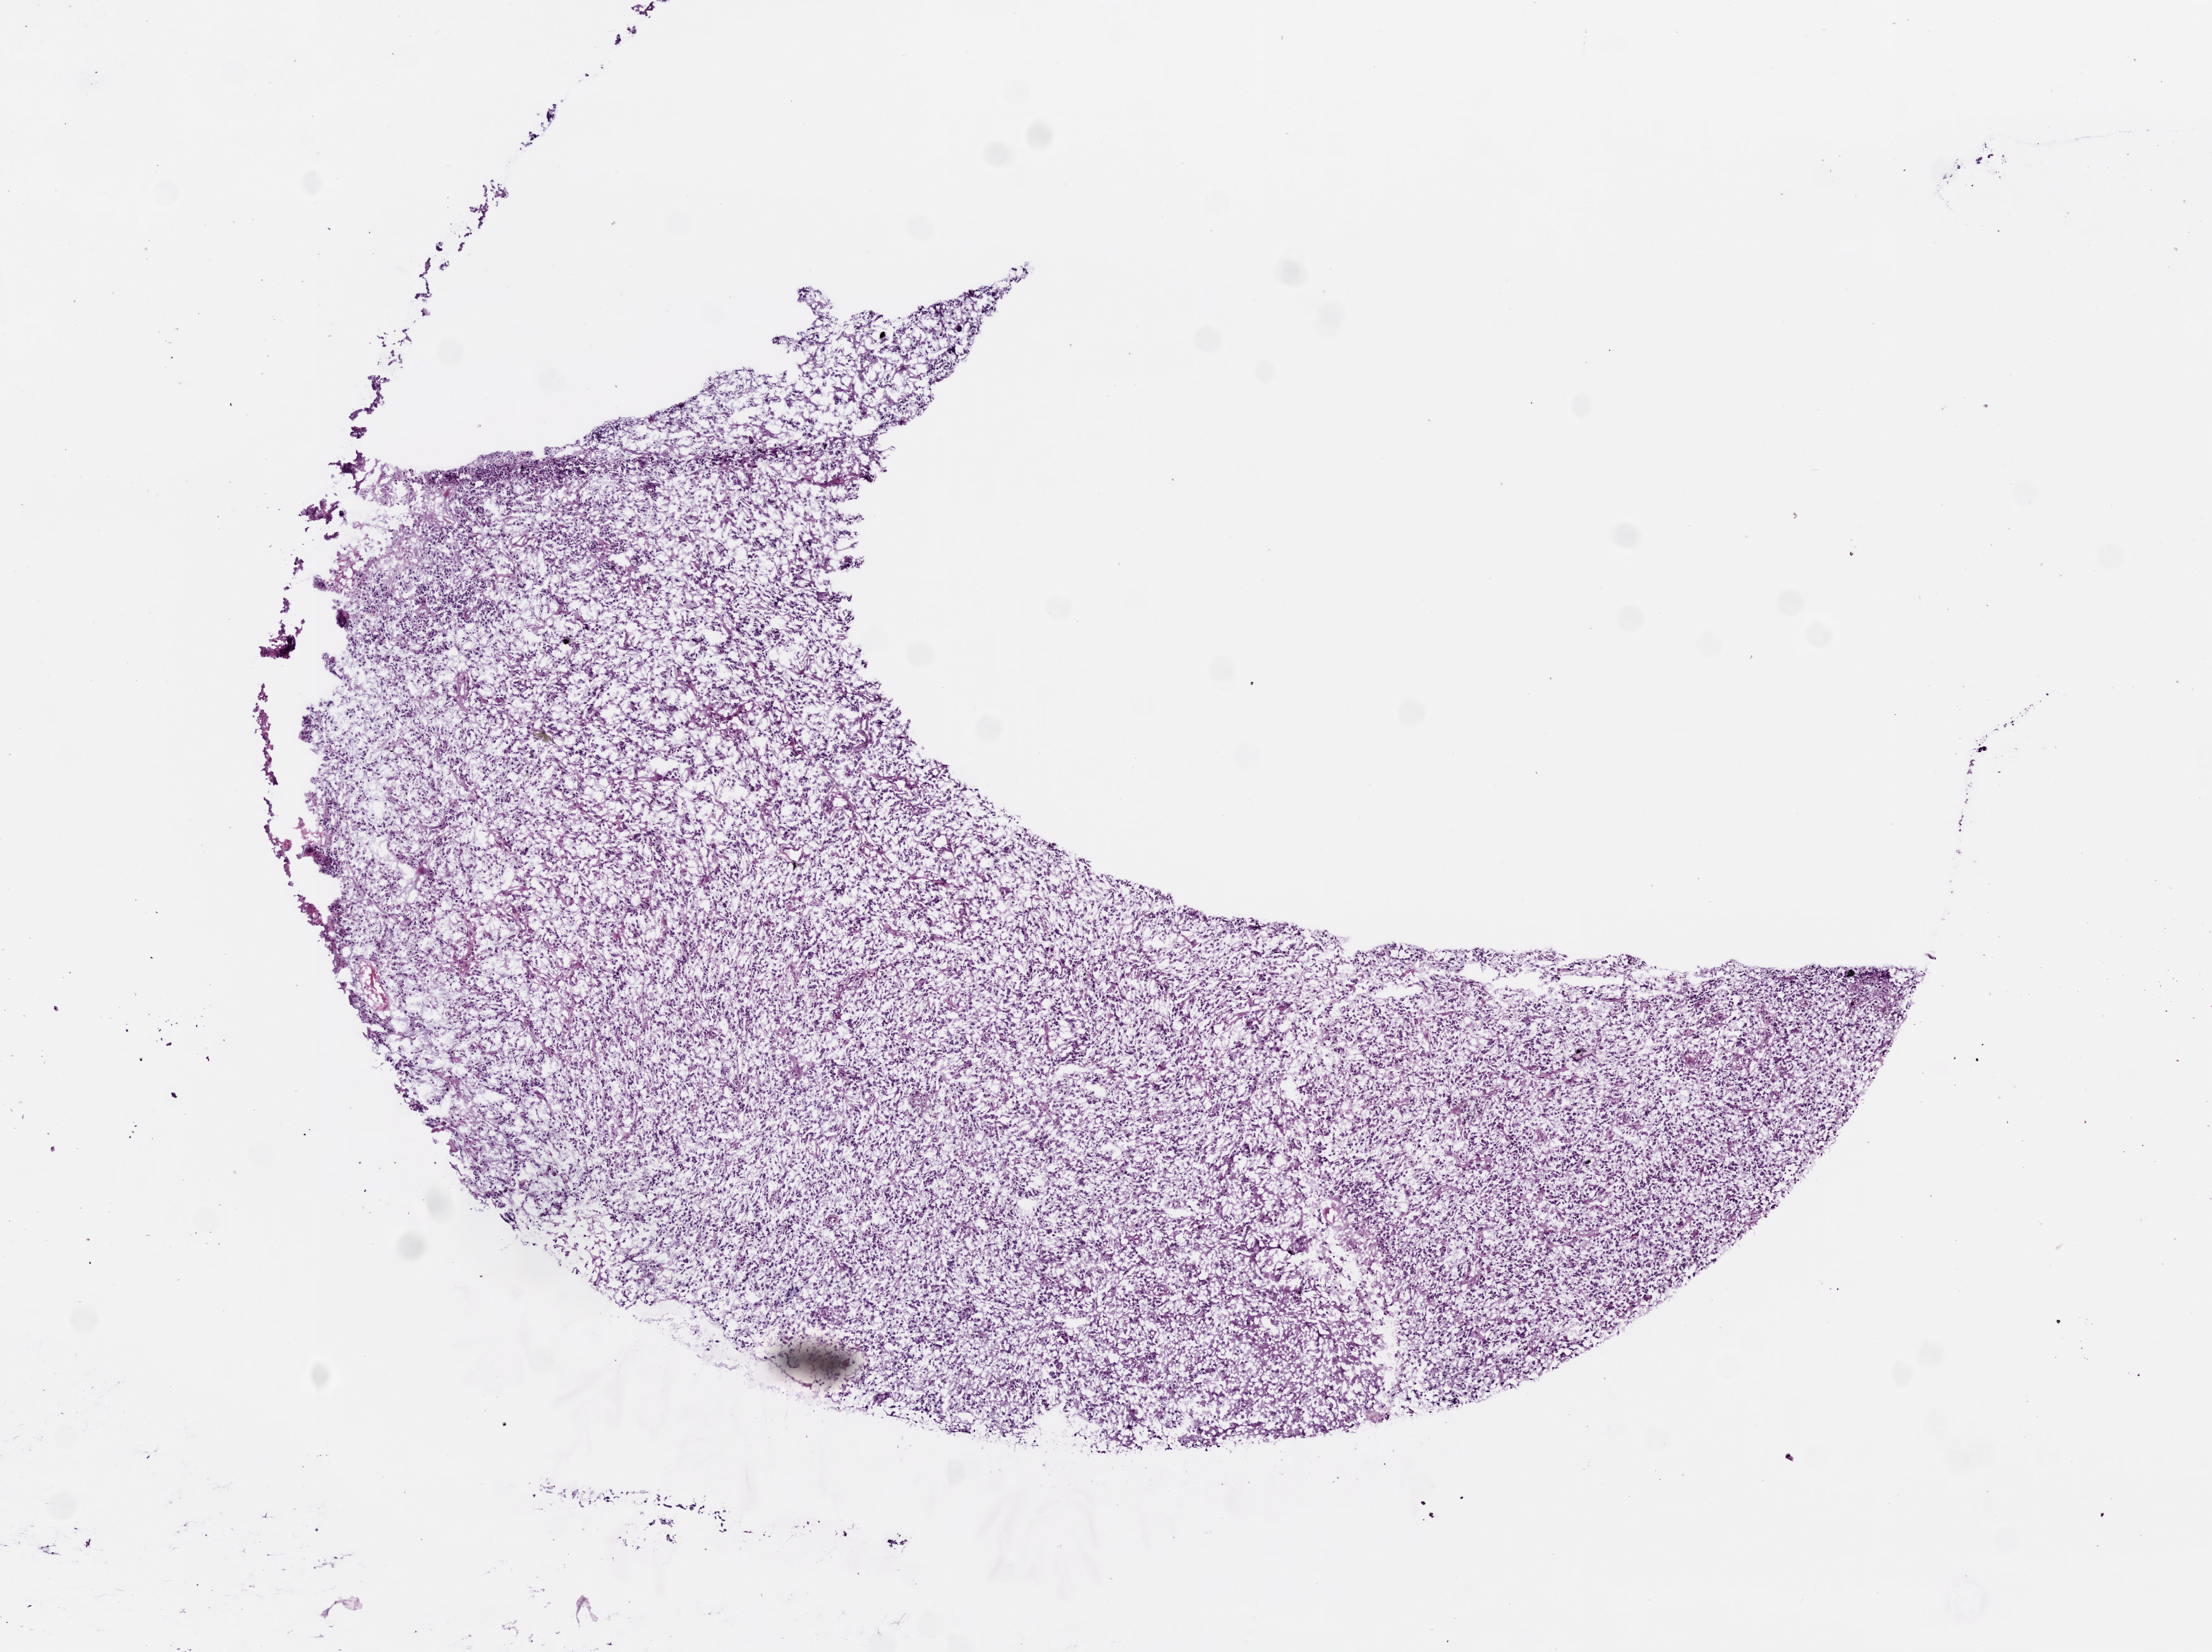
Digitized Hematoxylin and eosin (H&E) stained tissue section (whole slide) — a low-resolution overview of the entire scanned area, about 7.0 x 5.2 mm (acquisition: 20x scan); frozen section from the bottom of the tissue portion; brain, primary tumour sample. Patient: female, age at initial diagnosis 52 years. Composition of this section per pathologist review: tumour cells 98%, tumour nuclei 85%, normal cells 0%, stromal cells 0%, necrosis 2%.
• diagnosis: Glioblastoma